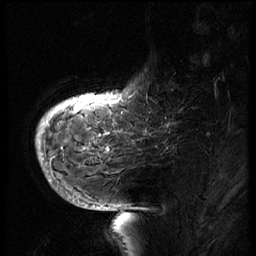
Breast MRI (dynamic contrast-enhanced), one sagittal slice; position 13 of 66 along the scan axis; 3 images stored at this slice position (order not interpretable as contrast timing); 1.5 T; TE 4.2 ms, TR 8.9 ms; 2.5 mm slice thickness; 256 × 256 image matrix, field of view 200 × 200 mm. Patient: female, 56 years. Case-level facts recorded for this patient, not image findings: setting: breast cancer imaged before/during neoadjuvant chemotherapy.
Outlined on this slice (semi-automatically segmented with operator editing):
- analysis volume of interest (the breast-tissue region the enhancement analysis was run in; not a lesion): bounding box <129,62,194,127> (left, top, right, bottom; pixels)
- tumour enhancement mask (voxels above the 140 % enhancement threshold inside the analysis volume of interest): <139,122,173,127>